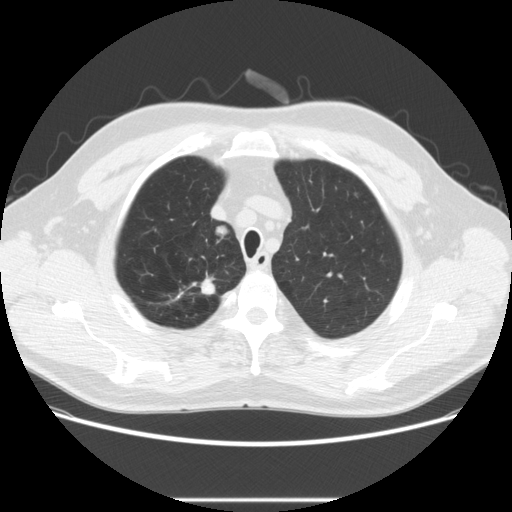
Axial slice from a low-dose chest CT screening exam, baseline screening round, lung window (W 1500 / L -600 HU), 2.5 mm slice thickness, standard (soft-tissue) reconstruction kernel (STANDARD), slice 42 of 270 in the series. Male, age 64 years at enrolment. Former smoker at enrolment.
2 lesions marked by an expert reader on this slice (largest first), bounding box <171,276,223,306> (left, top, right, bottom; pixels); <210,220,236,245>. The screening reader recorded 2 non-calcified nodules or masses ≥4 mm on this exam; which of them these boxes mark is not recorded. Official screen result: positive, change unspecified: nodule(s) >= 4 mm or enlarging nodule(s), mass(es), or other non-specific abnormalities suspicious for lung cancer.